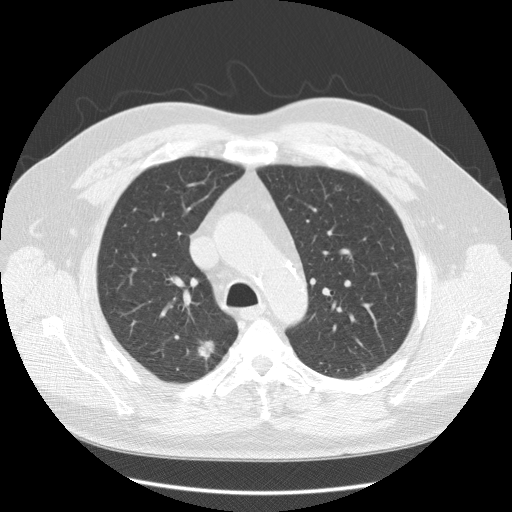
Low-dose screening chest CT, one axial slice; reconstruction kernel STANDARD; lung window (W 1500 / L -600 HU); 2.5 mm slice thickness; 512 × 512 image matrix, field of view 380 × 380 mm.
Outlined on this slice (expert manual segmentation):
- lesion 1 (tumor, upper lobe of right lung): bounding box (x1, y1, x2, y2) in pixels: (198, 340, 214, 360)